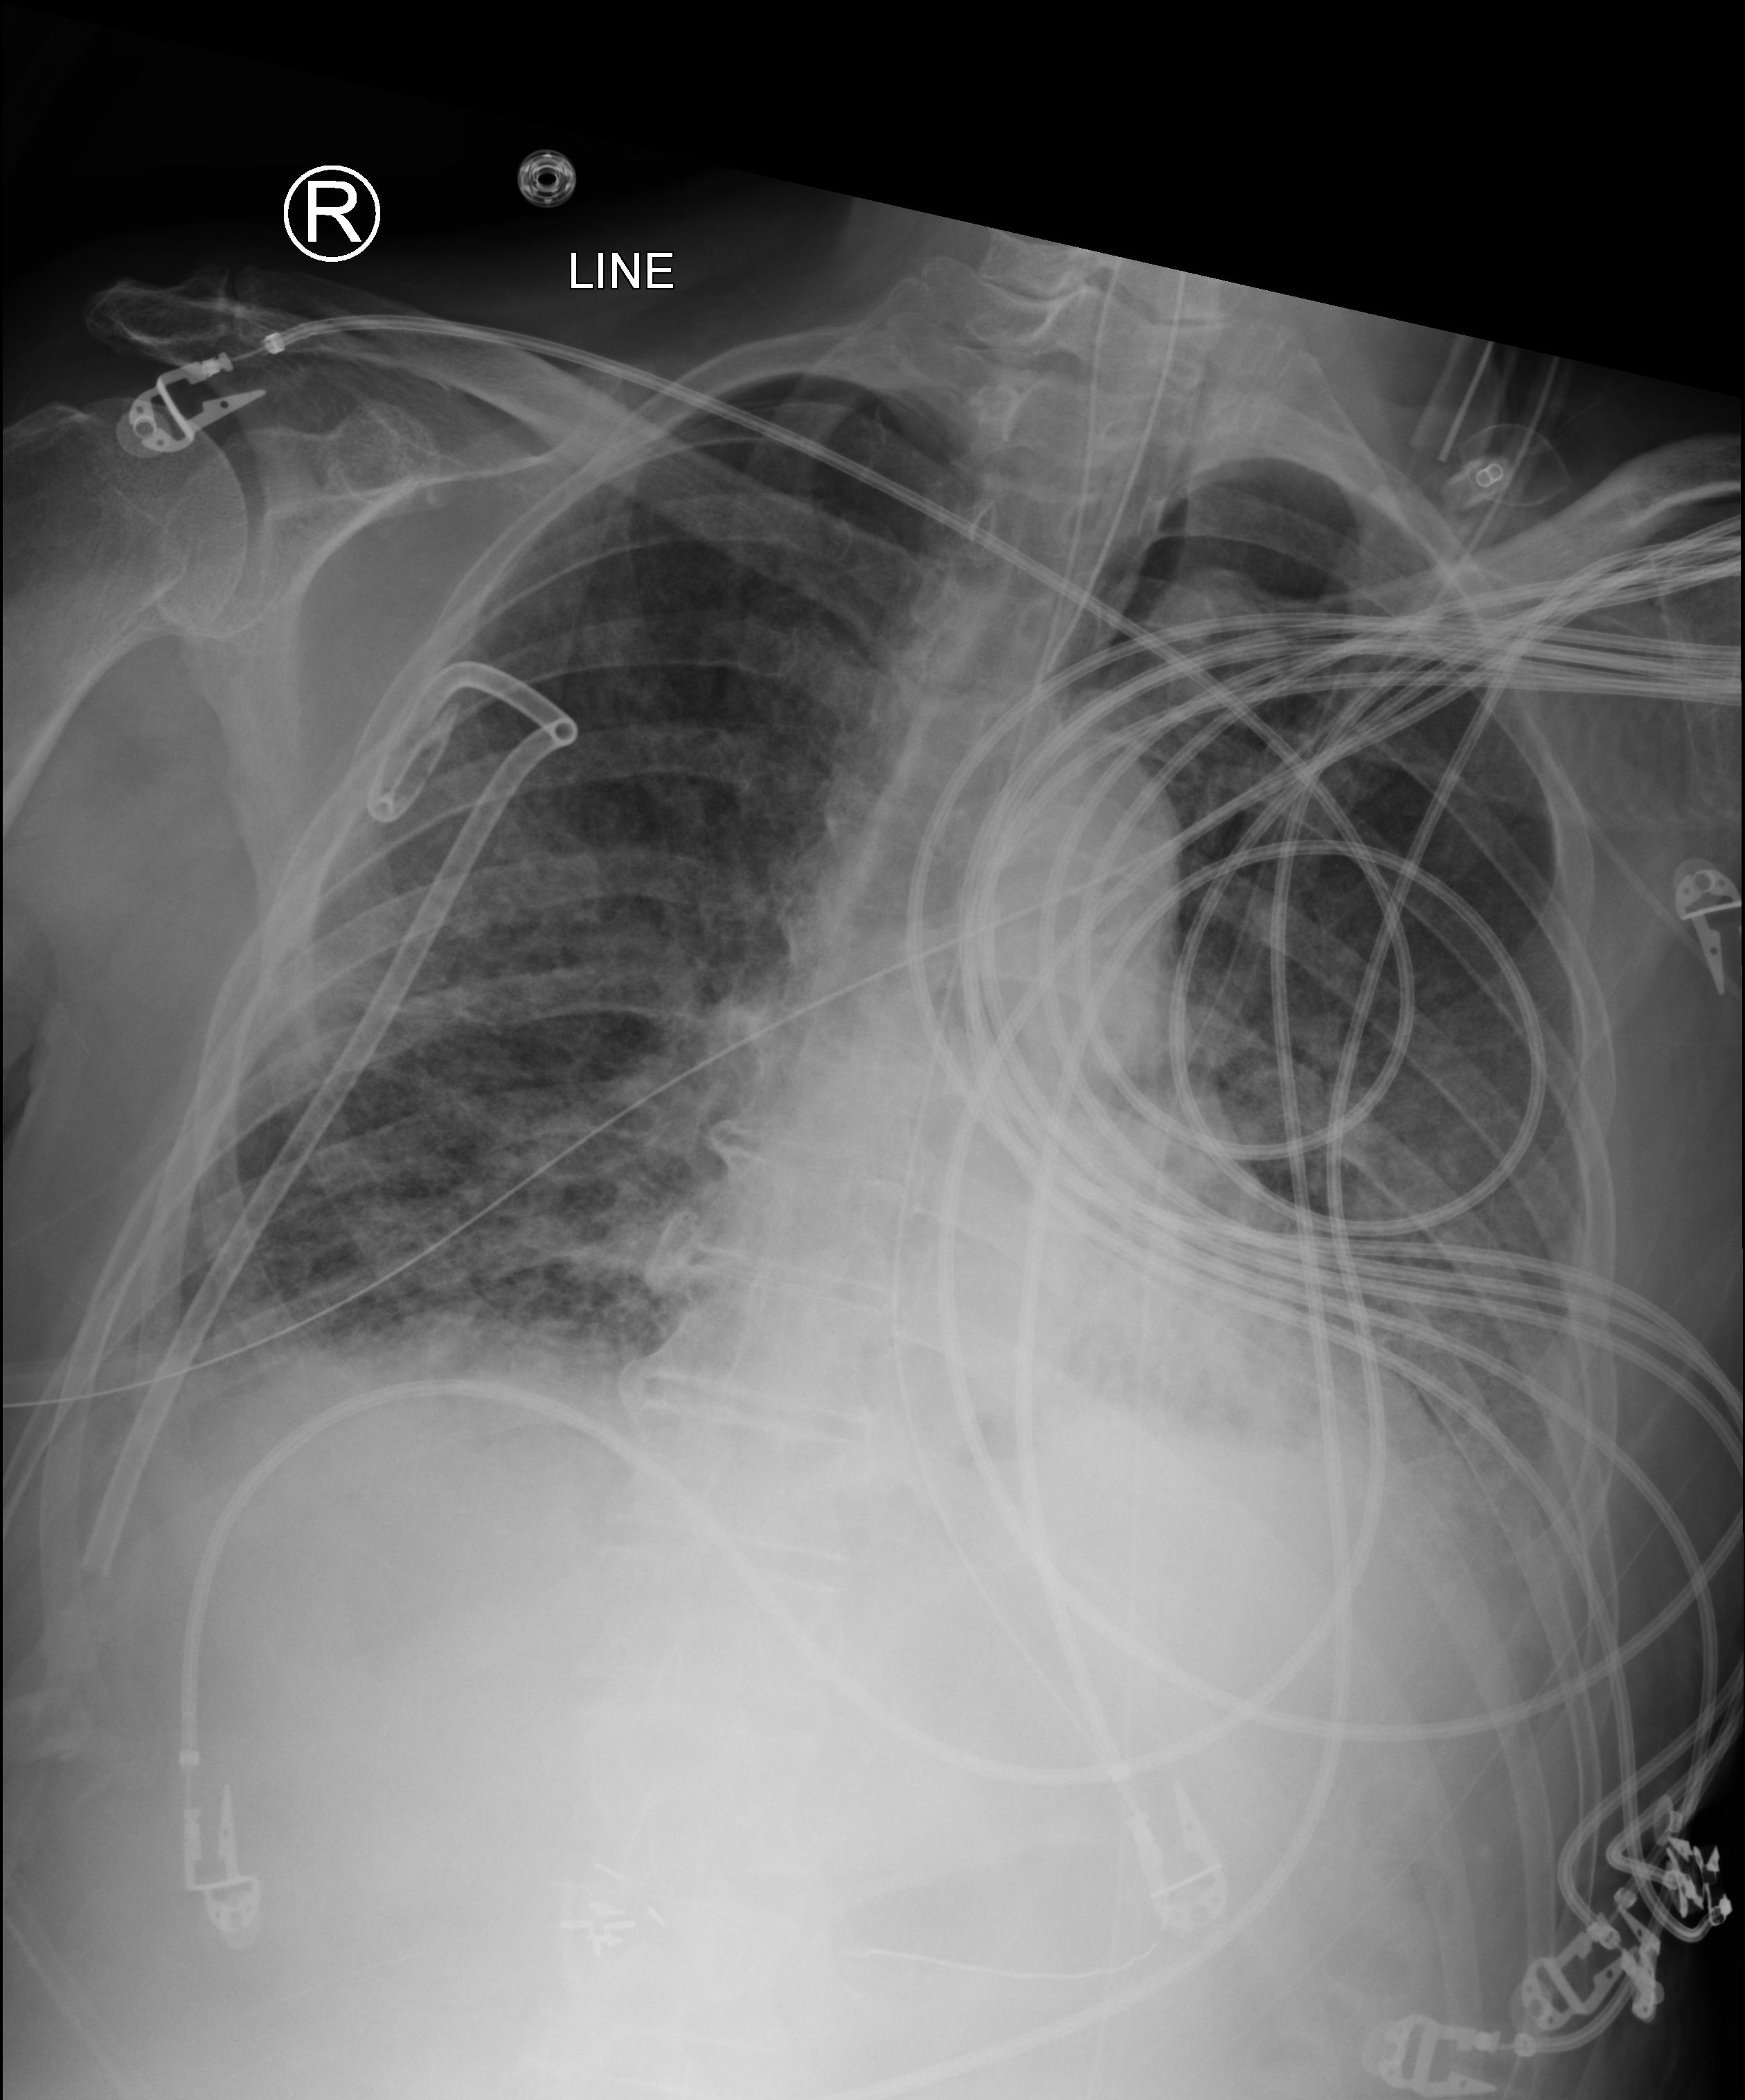
Bedside chest radiograph (computed radiography); anteroposterior (AP) projection. Patient hospitalised with COVID-19; male, aged 75–90 years.
From the hospital-stay record, not from the radiograph (when in the stay this image was taken is not recorded): mechanically ventilated during this hospital stay: yes.